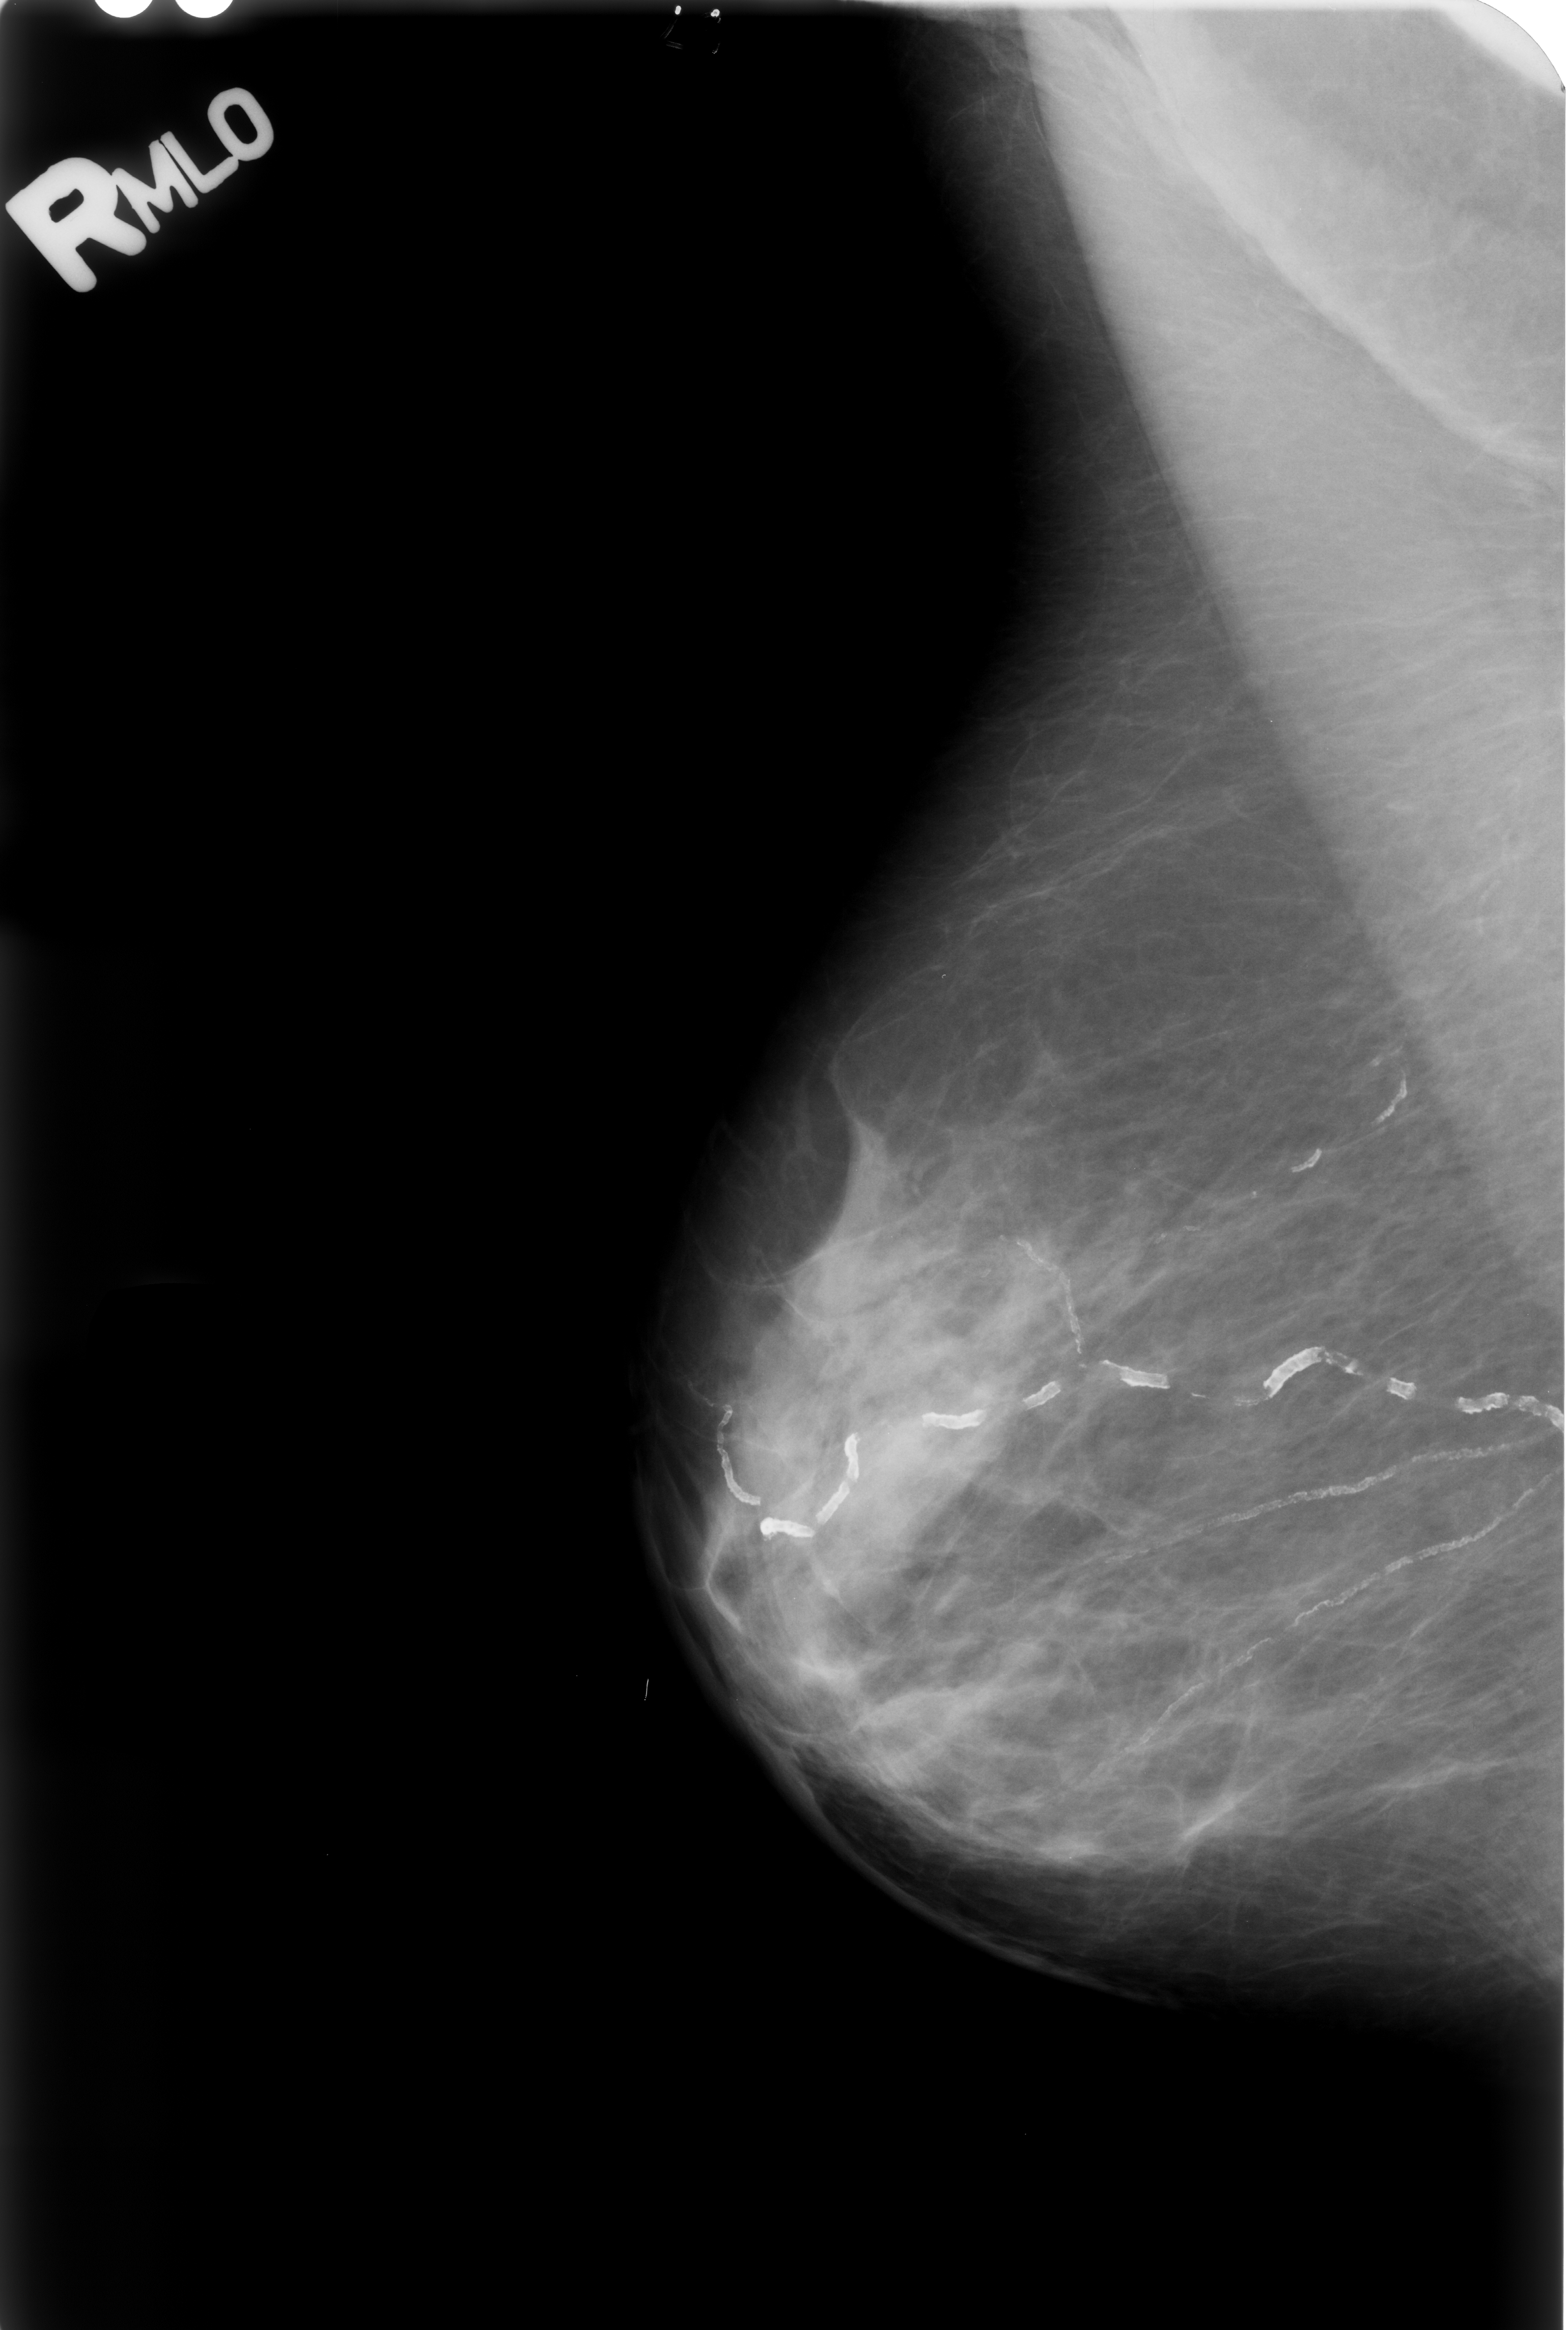
Mammogram (digitized film); right breast; MLO view.
- Marked abnormality: calcifications, morphology vascular; BI-RADS assessment category 2; benign without callback (not worked up further).